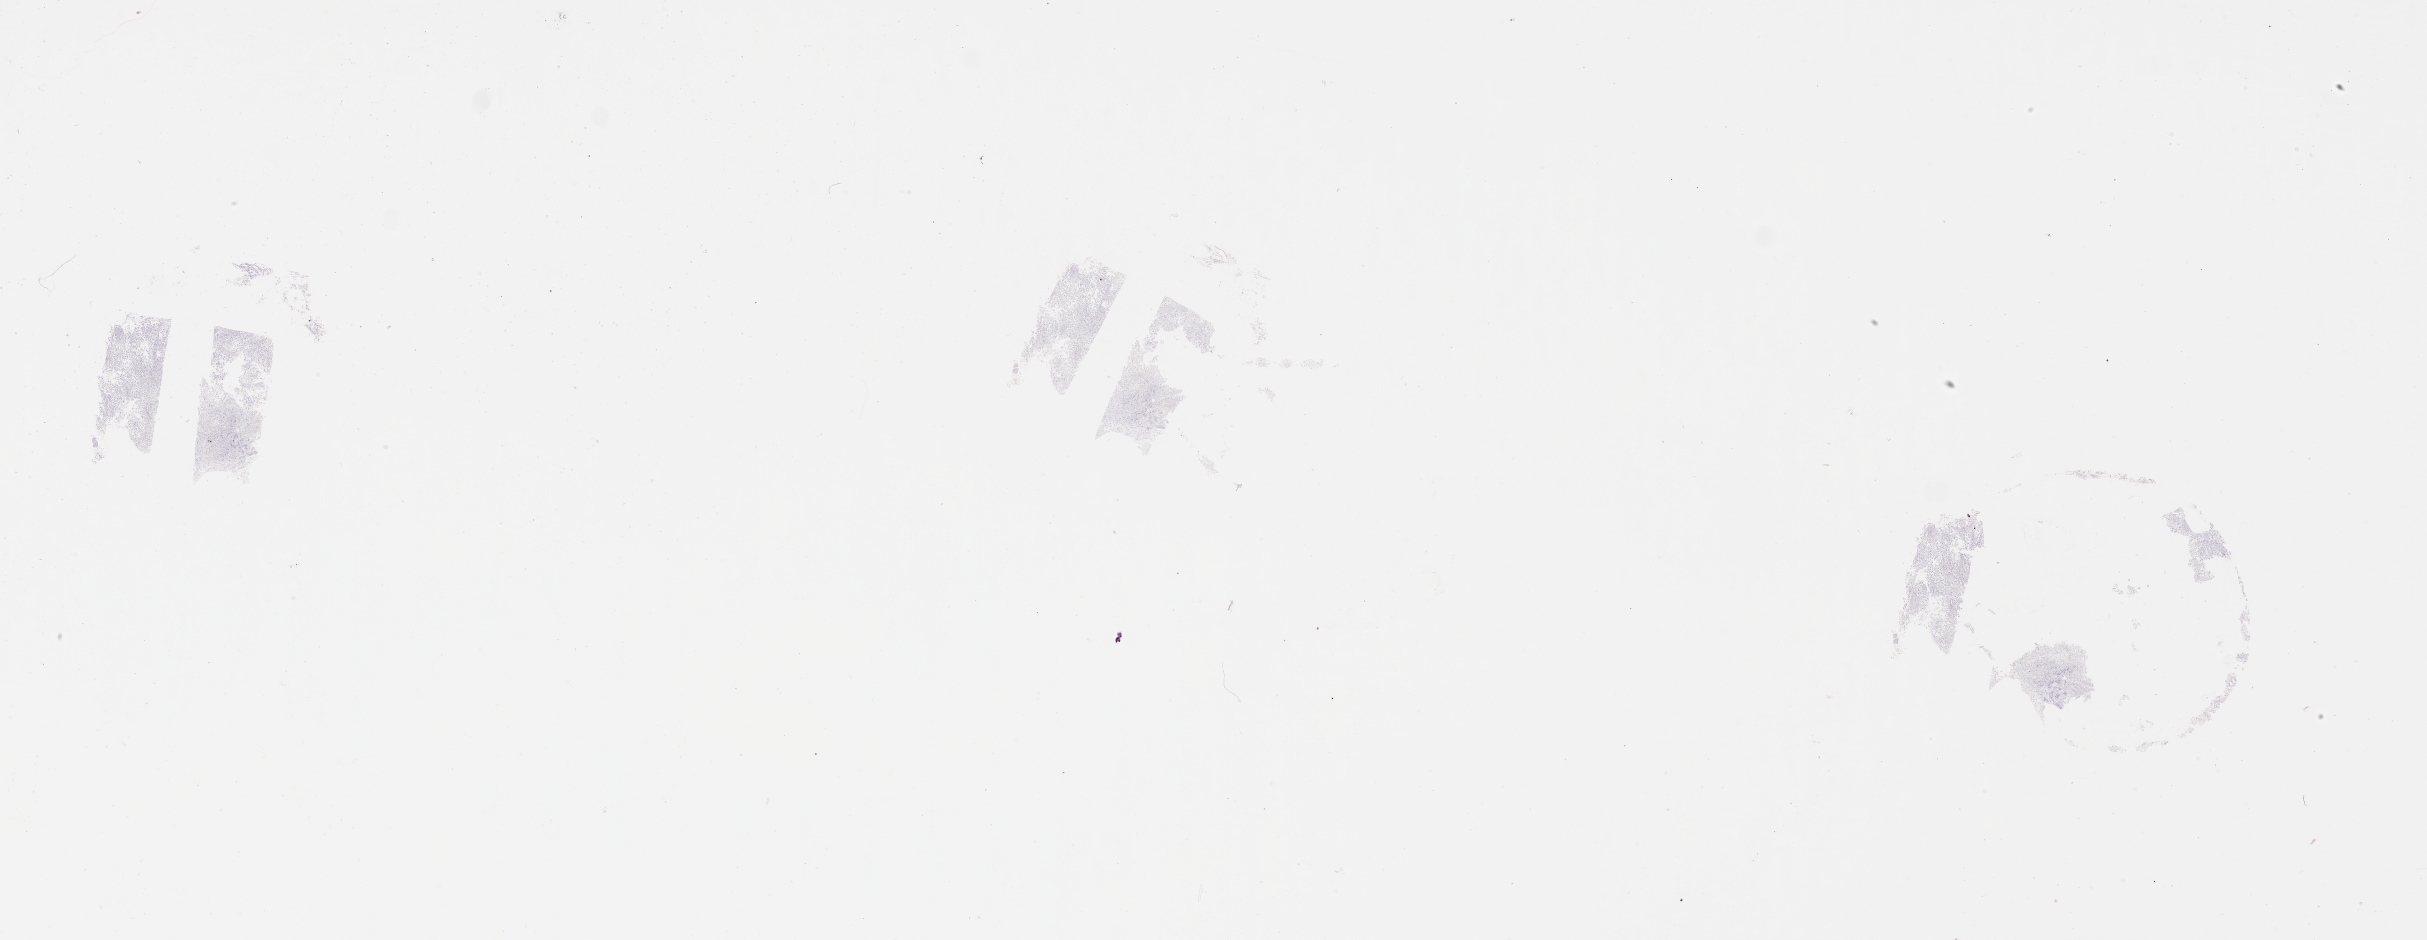
H&E whole-slide image, whole scanned area (about 39.1 x 15.1 mm, slide scanned at 20x) shown as a low-resolution overview, tumour tissue sample, sampled site: brain. Male, 65 y/o. Pathologist review of this section (percent, as recorded): tumour nuclei 70%, necrosis 10%.
- primary tumour site (as recorded): parietal lobe
- histologic diagnosis: Glioblastoma